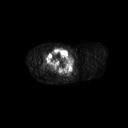
FDG PET of an extremity soft-tissue mass (from a PET/CT study), one axial slice; slice 263 of 311 in the series (ordered by position); 3.27 mm slice thickness; 128 × 128 image matrix, field of view 700 × 700 mm. Male patient, age 50 years. From the clinical record (not read from this slice): histological type: undifferentiated - pleiomorphic; grade: high; site of the primary tumour: right thigh.
Annotated regions visible in this slice (expert contour drawn on MRI and transferred to this co-registered scan by the dataset authors):
- gross tumour volume including surrounding oedema: bounding box <45,47,67,68> (left, top, right, bottom; pixels)
- gross tumour volume (mass): <46,48,67,68>